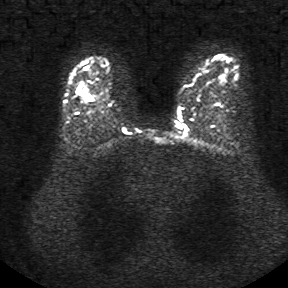
Breast MRI, one axial slice. Position 27 of 34 along the scan axis. Diffusion-weighted series; image 2 of 4 stored at this slice position (different b-values; order by instance number). 1.5 T. 288 × 288 image matrix, field of view 340 × 340 mm. Female patient.
Annotated regions visible in this slice (manually delineated by an expert):
- tumour on diffusion-weighted imaging: bounding box <77,91,92,100> (left, top, right, bottom; pixels)